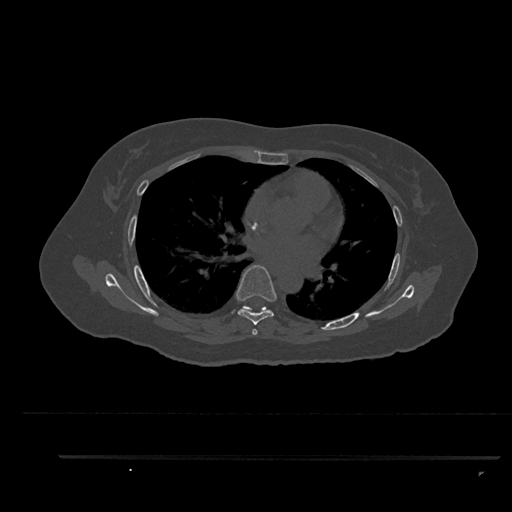
CT including the spine, one axial slice; slice 551 of 797 in the series (ordered by position); reconstruction kernel Br40s/3; 120 kVp; bone window (W 1800 / L 400 HU); 512 × 512 image matrix, field of view 408 × 408 mm. Patient: female, 44 years. From the clinical record (not read from this slice): primary cancer: renal; vertebrae with lytic lesions (as recorded): L1.
Structures marked on this image (semi-automatic segmentation, software-assisted and operator-edited):
- T6 vertebra: box from (x=236, y=265) to (x=277, y=335) px
- T7 vertebra: (x=246, y=306)–(x=263, y=313)